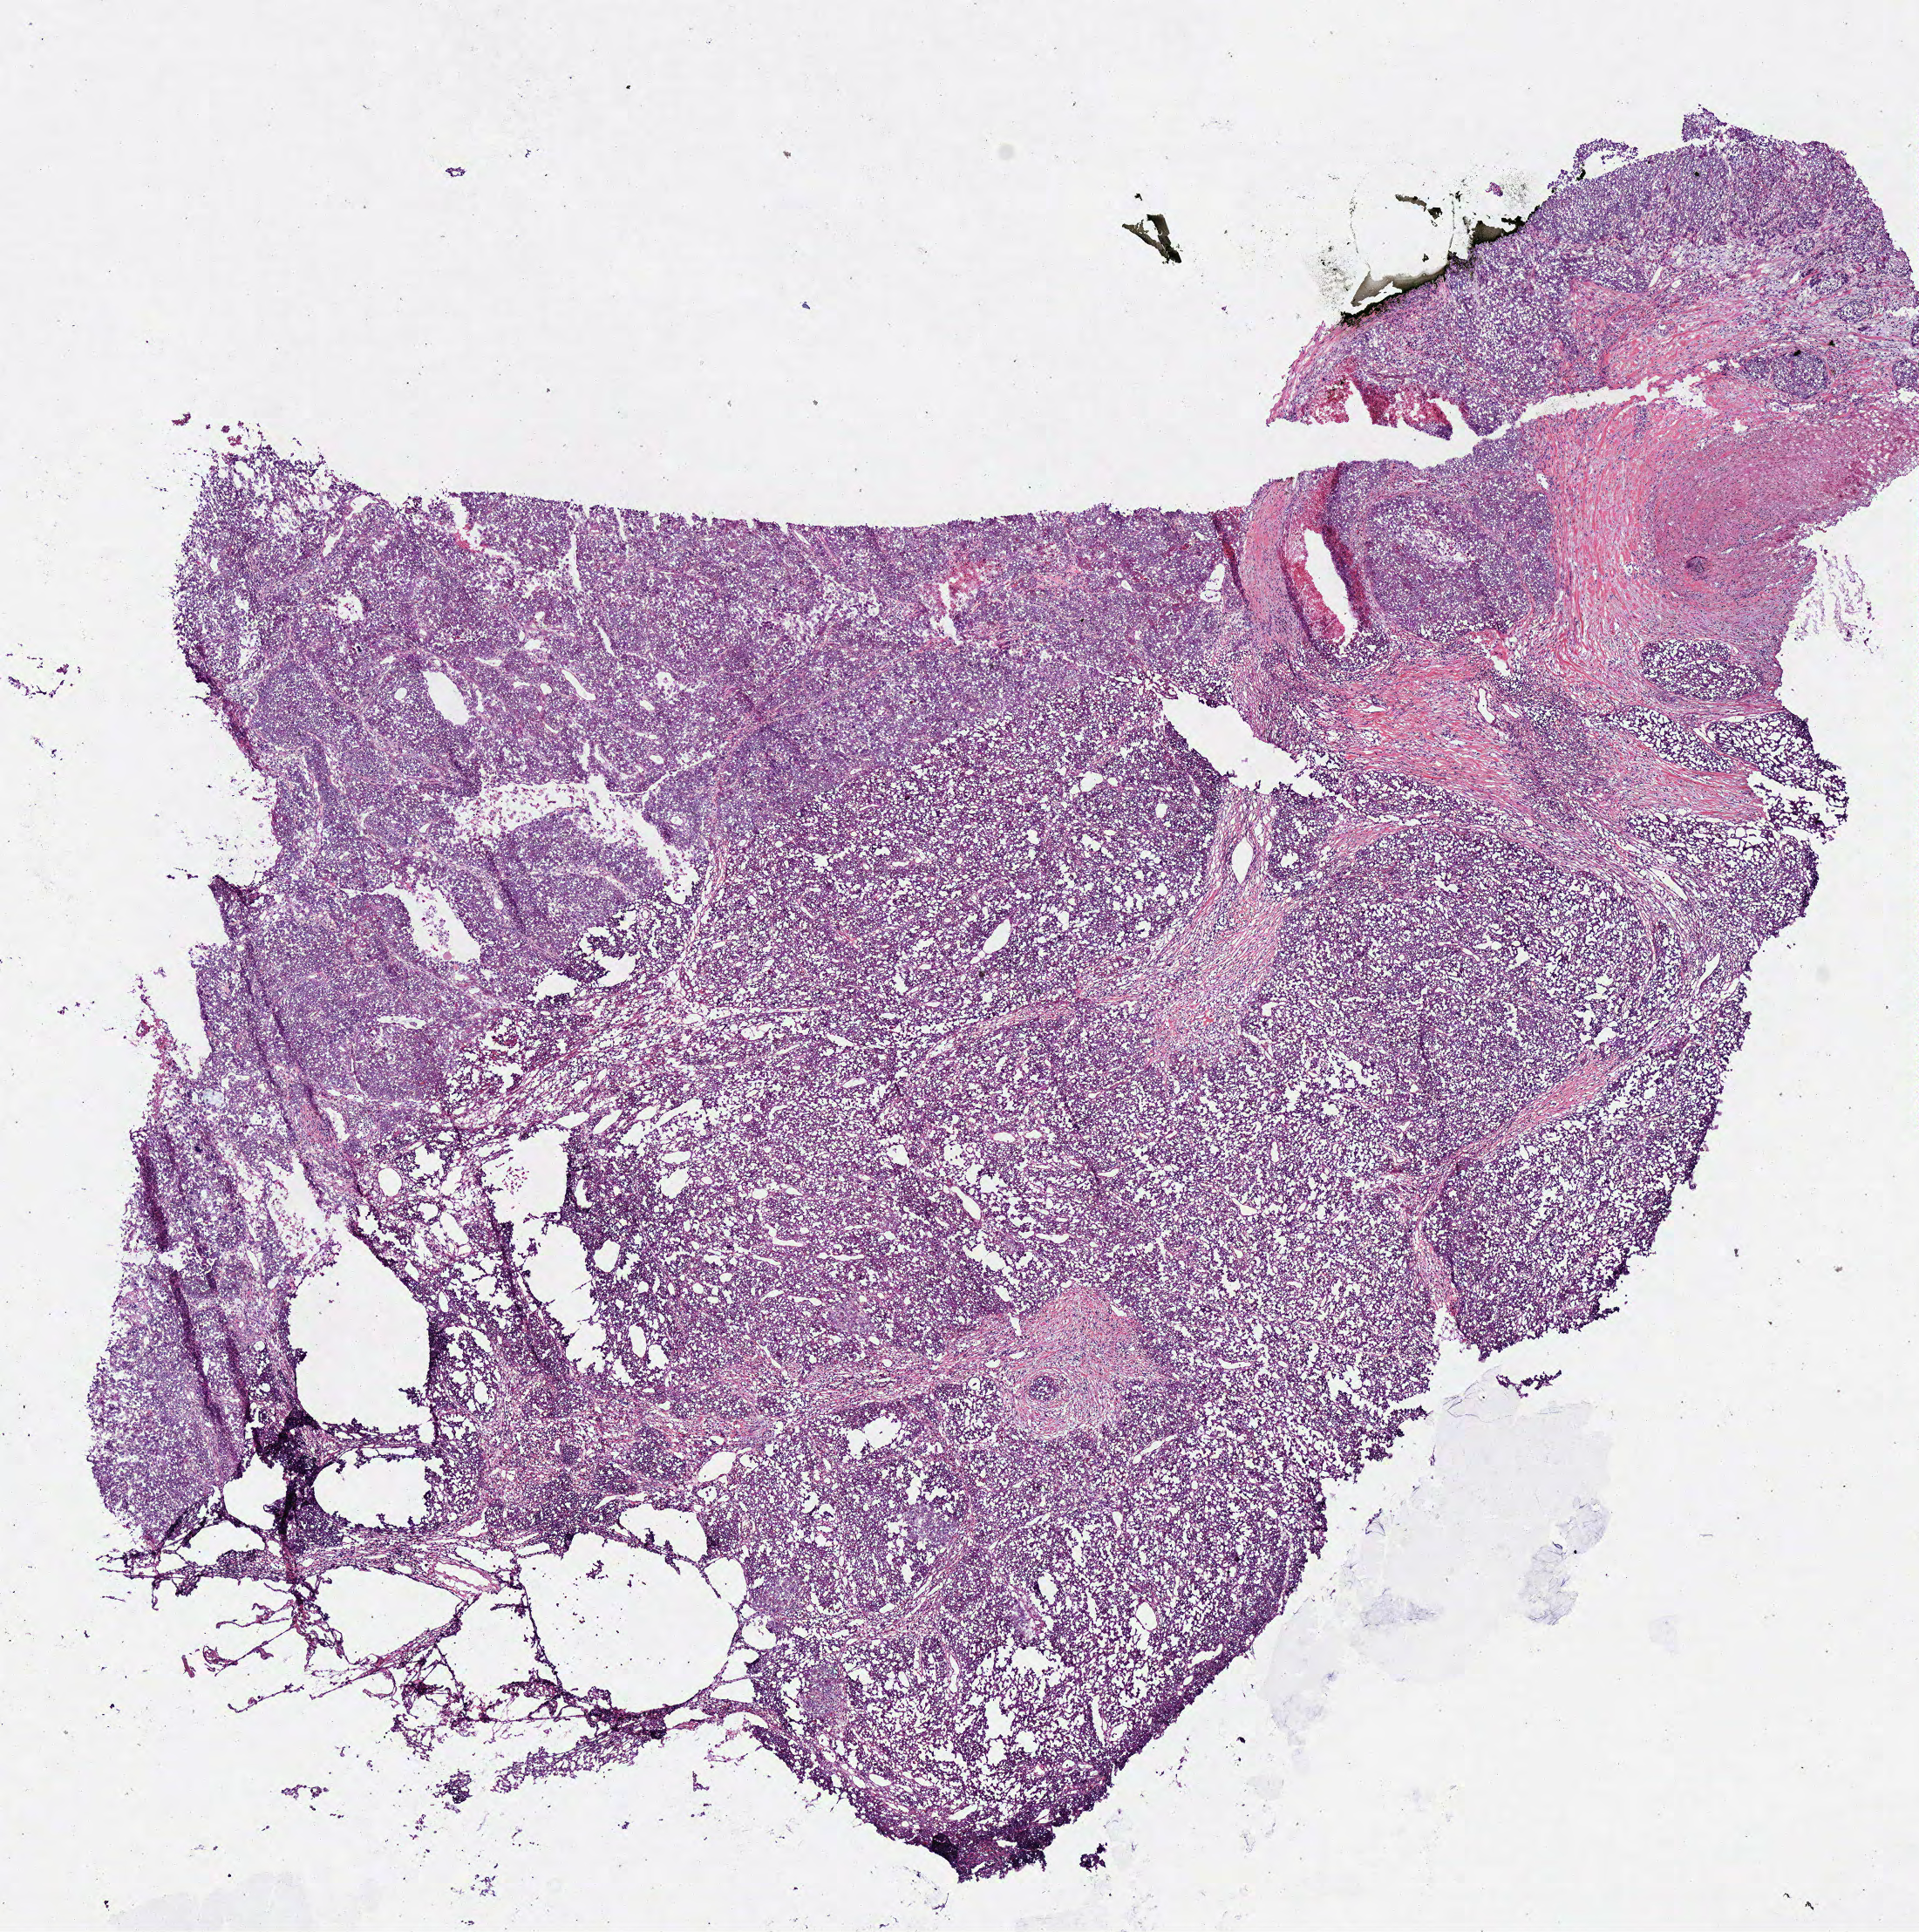
Whole-slide histology image, H&E, shown as a low-resolution overview of the whole scanned area (about 8.7 x 8.7 mm, slide scanned at 40x); frozen section from the bottom of the tissue portion; lung, primary tumour sample. Patient: male, age at initial diagnosis 74 years. Composition of this section per pathologist review: tumour cells 82%, tumour nuclei 85%, normal cells 0%, stromal cells 15%, necrosis 3%.
- pathologic diagnosis: Squamous cell carcinoma, NOS (upper lobe, lung)
- AJCC pathologic stage: IIA